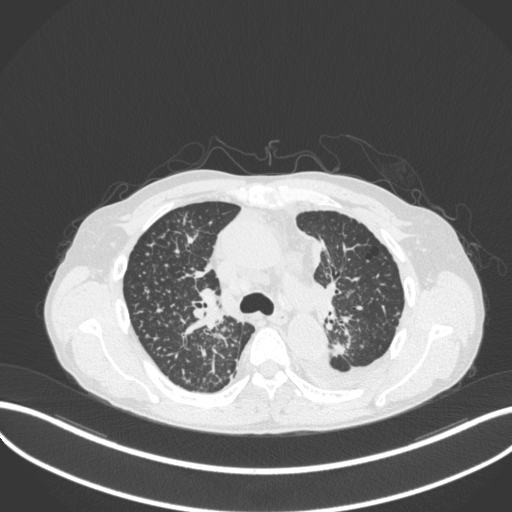
Chest CT, one axial slice; position 244 of 319 along the scan axis; reconstruction kernel B31f; 120 kVp; lung window (W 1500 / L -600 HU); 1 mm slice thickness; 512 × 512 image matrix, field of view 400 × 400 mm. Male patient, age 58 years. From the clinical record (not read from this slice): clinical TNM (as recorded): T1c N3 M1.
Outlined on this slice (rectangle marked by the reading radiologist):
- lung tumour (recorded histology: adenocarcinoma): box from (x=330, y=340) to (x=348, y=359) px